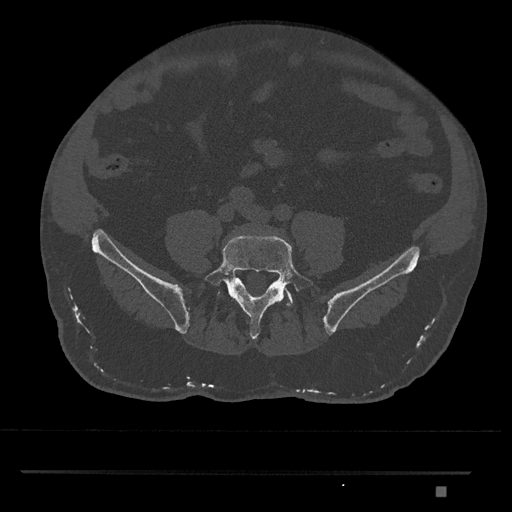
CT including the spine, one axial slice. Slice 558 of 1134 in the series (ordered by position). Reconstruction kernel Br40s/3. Bone window (W 1800 / L 400 HU). 512 × 512 image matrix. Patient: male, 65 years. From the clinical record (not read from this slice): primary cancer: prostate.
Annotated regions visible in this slice (semi-automatically segmented with operator editing):
- L5 vertebra: bounding box <204,235,316,340> (left, top, right, bottom; pixels)